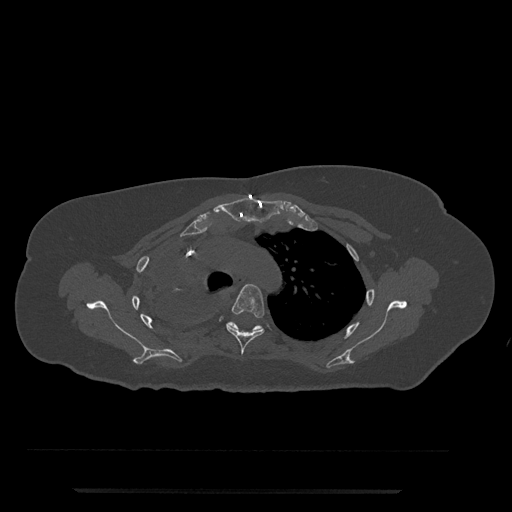
CT including the spine, one axial slice; slice 580 of 797 in the series (ordered by position); reconstruction kernel Br40s/3; 120 kVp; bone window (W 1800 / L 400 HU); 0.5 mm slice thickness; 512 × 512 image matrix, field of view 440 × 440 mm. Female patient, age 51 years. Case-level facts recorded for this patient, not image findings: primary cancer: neuro; vertebrae with lytic lesions (as recorded): T8.
Outlined on this slice (semi-automatically segmented with operator editing):
- T4 vertebra: bounding box (x1, y1, x2, y2) in pixels: (226, 284, 265, 355)
- T5 vertebra: (226, 322, 264, 333)